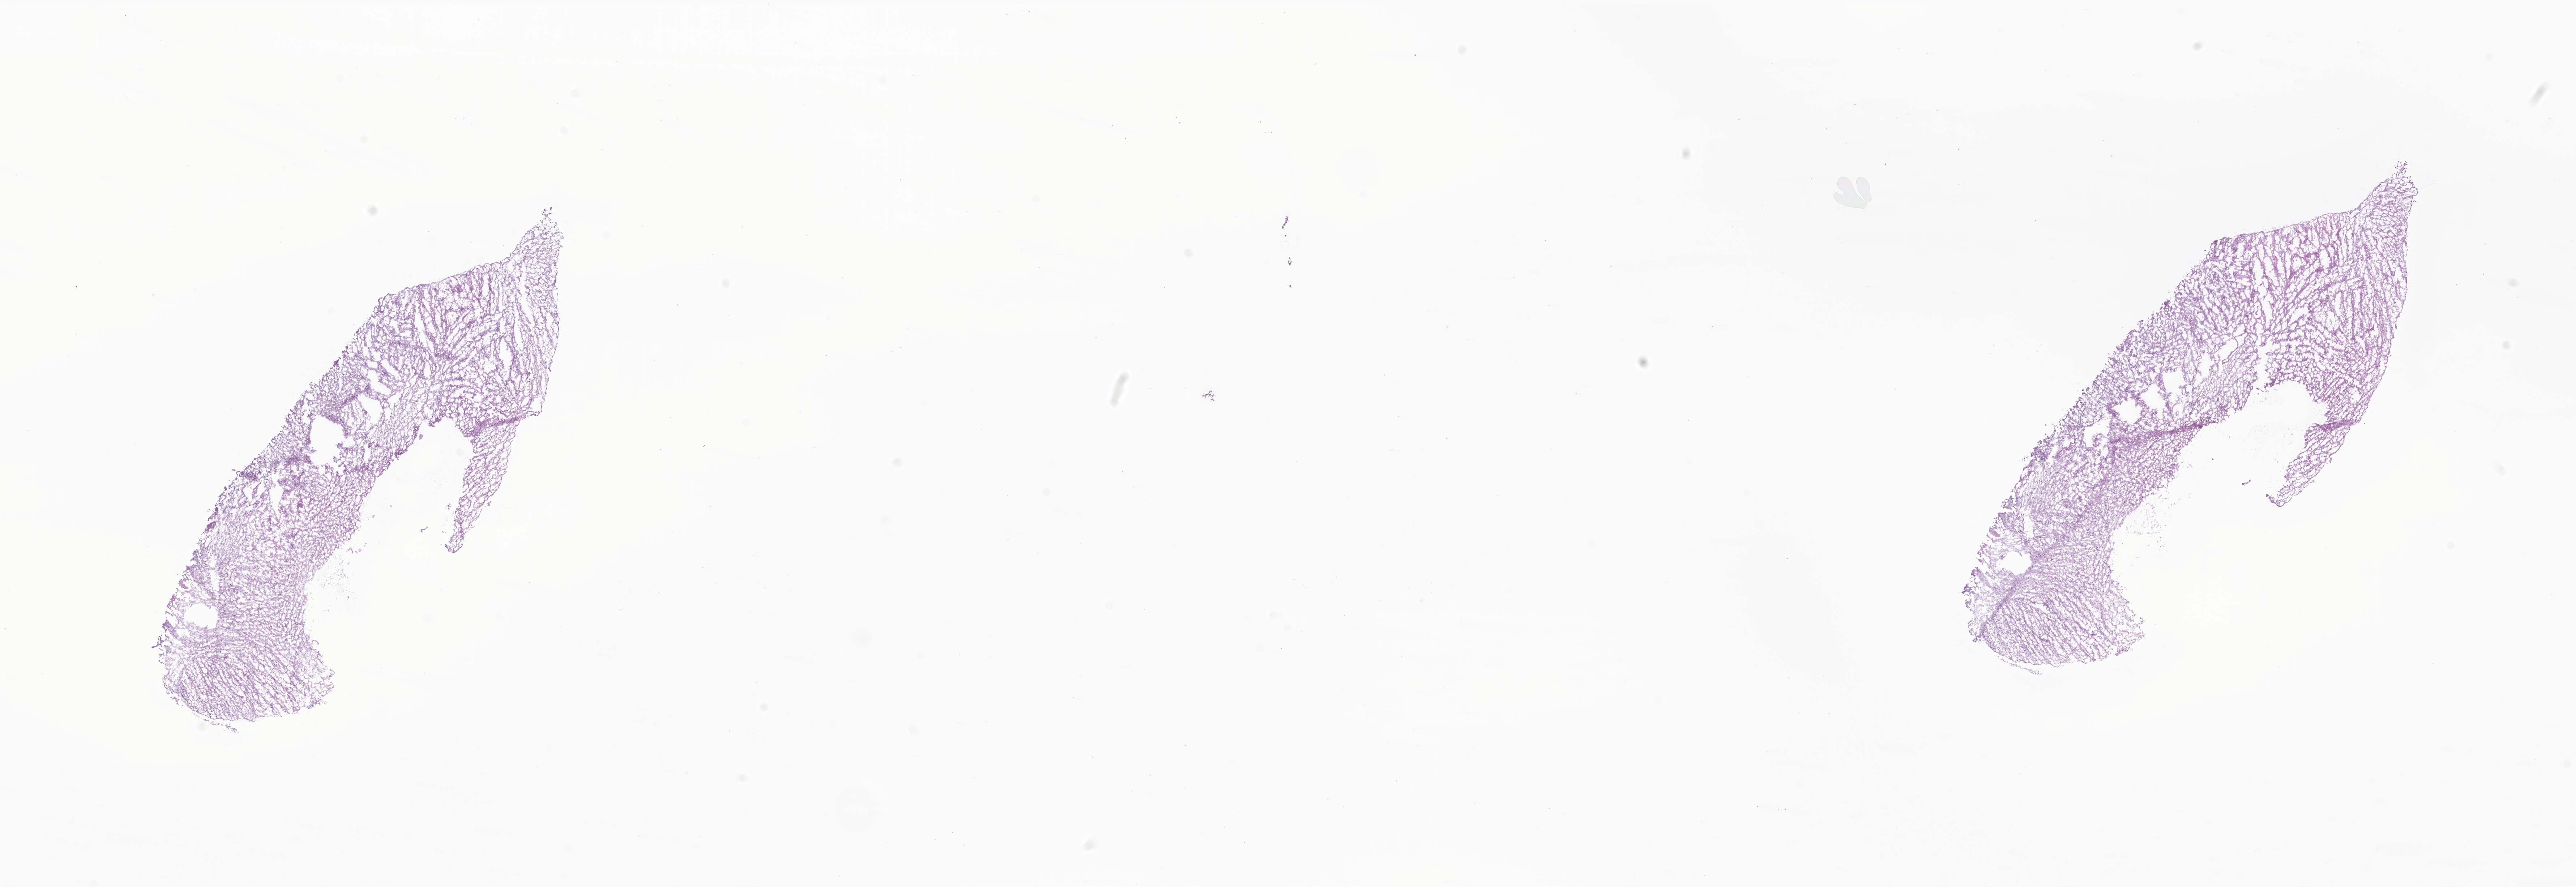
Whole-slide image, hematoxylin and eosin (H&E) stain of tumor tissue from the brain stem — shown as a low-resolution overview of the whole scanned area (about 30.0 x 10.3 mm). Frozen section. Patient female; age 145 months (12 years 1 month).
- recorded diagnosis: Glioma, malignant